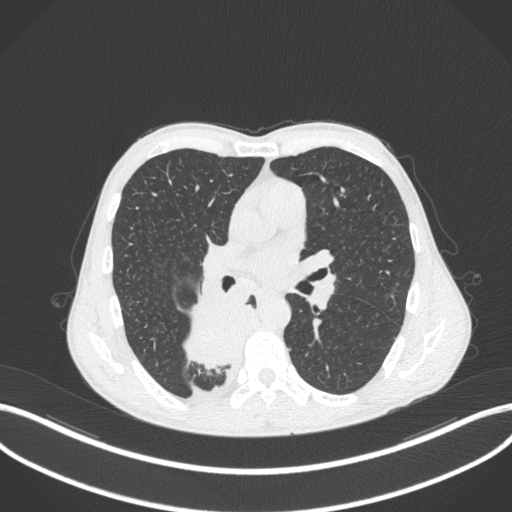
Chest CT, one axial slice; position 207 of 371 along the scan axis; reconstruction kernel B31f; 120 kVp; lung window (W 1500 / L -600 HU); 1 mm slice thickness; 512 × 512 image matrix, field of view 400 × 400 mm. Male patient, age 58 years. From the clinical record (not read from this slice): clinical TNM (as recorded): T3 N1 M1.
Structures marked on this image (bounding box drawn by a radiologist):
- lung tumour (recorded histology: squamous cell carcinoma): bounding box <176,293,251,369> (left, top, right, bottom; pixels)